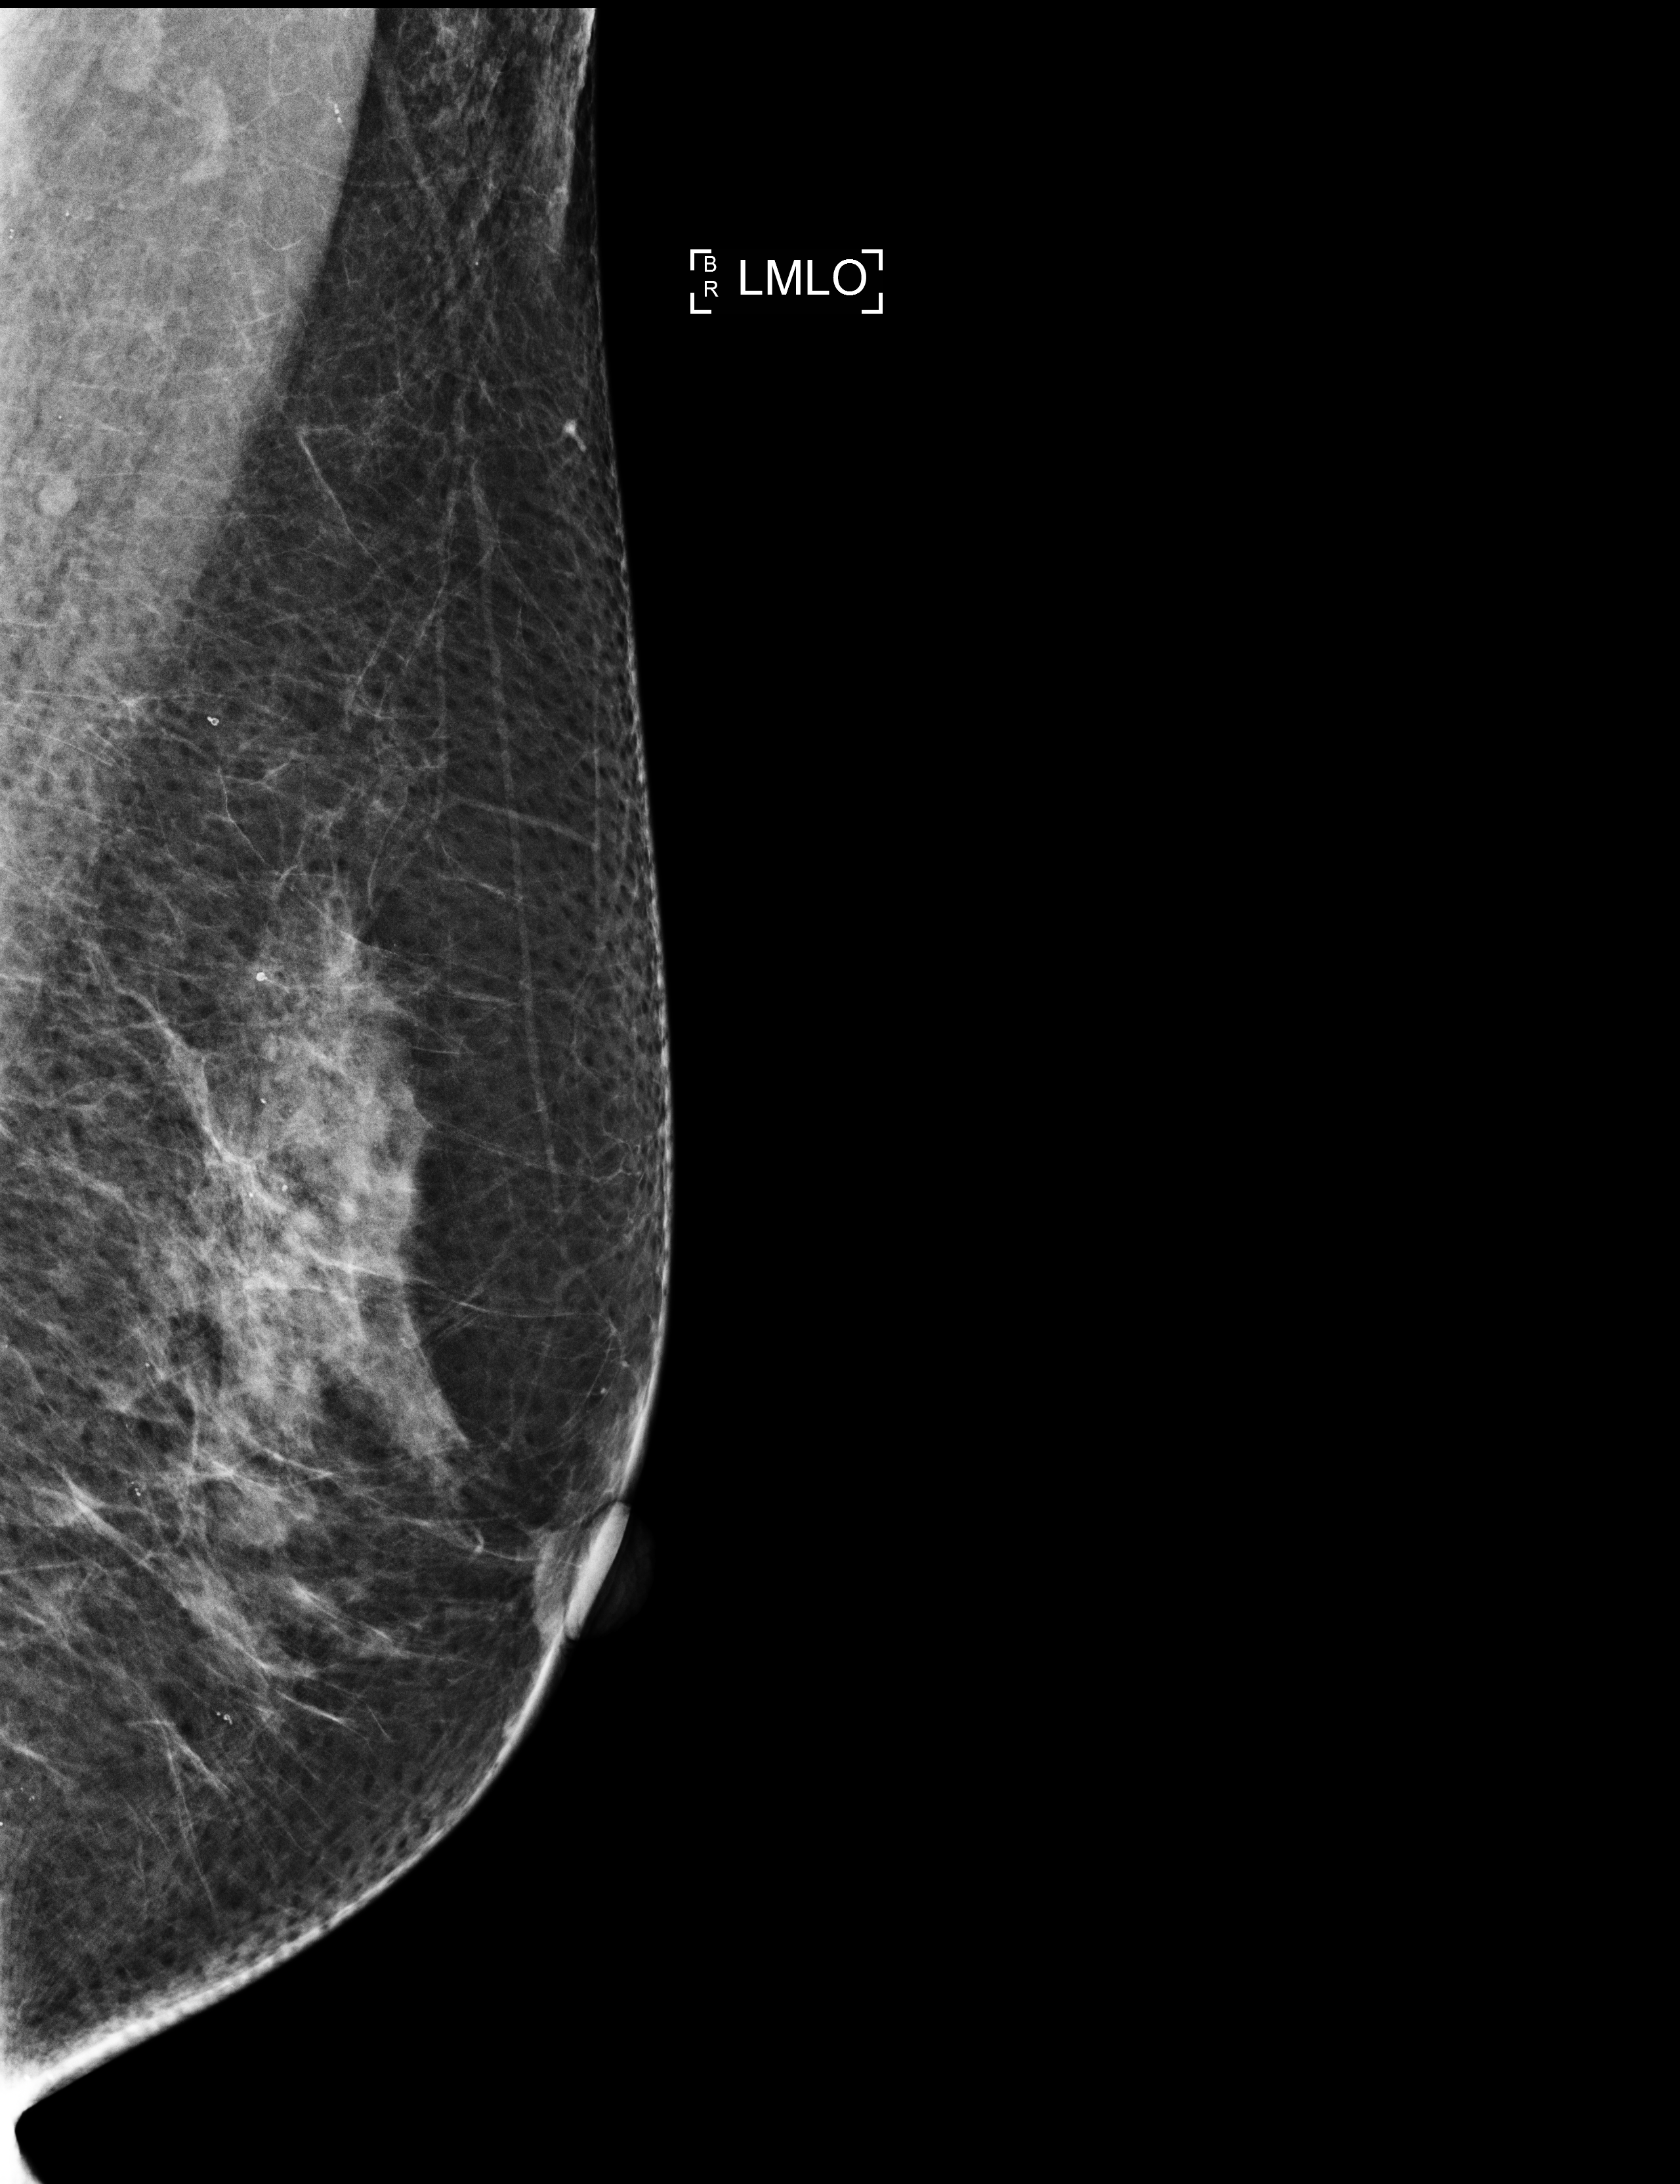
Screening examination, compressed breast thickness 59 mm. Patient: female, 69 years.
Image type: full-field digital mammogram. Breast: left. Projection: medio-lateral oblique projection.